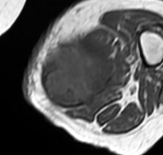
MRI of an extremity soft-tissue mass, one axial slice. Position 22 of 65 along the scan axis. MR volume resampled by the dataset authors to the PET/CT grid (not the native acquisition matrix). 3.27 mm slice thickness. 163 × 155 image matrix, field of view 159 × 151 mm. Female patient. Case-level facts recorded for this patient, not image findings: histological type: pleomorphic leiomyosarcoma; grade: high; site of the primary tumour: left thigh.
Structures marked on this image (expert contour drawn on MRI and transferred to this co-registered scan by the dataset authors):
- gross tumour volume including surrounding oedema: bounding box [x1, y1, x2, y2] px = [42, 31, 125, 109]
- gross tumour volume (mass): [42, 45, 115, 109]